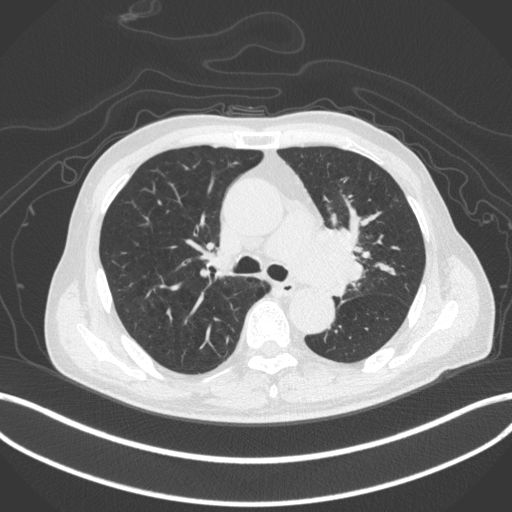
Chest CT, one axial slice. Slice 278 of 420 in the series (ordered by position). Reconstruction kernel B31f. 120 kVp. Lung window (W 1500 / L -600 HU). 512 × 512 image matrix. Patient: male, 77 years. From the clinical record (not read from this slice): clinical TNM (as recorded): T3 N1 M0.
Outlined on this slice (bounding box drawn by a radiologist):
- lung tumour (recorded histology: adenocarcinoma): bounding box (x1, y1, x2, y2) in pixels: (302, 224, 367, 303)